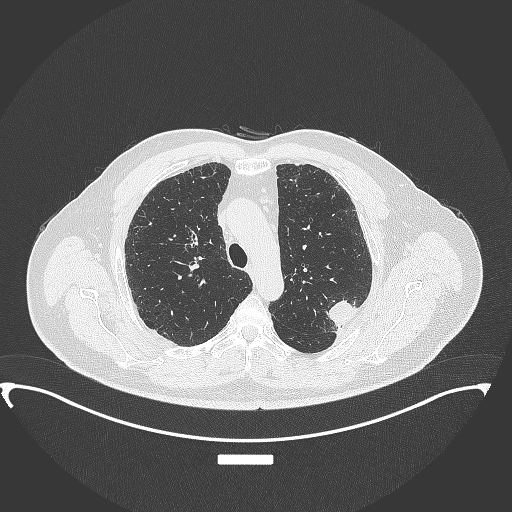
Chest CT, one axial slice; slice 266 of 350 in the series (ordered by position); reconstruction kernel B70f; lung window (W 1500 / L -600 HU); 1 mm slice thickness; 512 × 512 image matrix. Patient: male, 64 years. Case-level facts recorded for this patient, not image findings: clinical TNM (as recorded): T1c N1 M1.
Outlined on this slice (bounding box drawn by a radiologist):
- lung tumour (recorded histology: adenocarcinoma): bounding box [x1, y1, x2, y2] px = [326, 295, 363, 333]